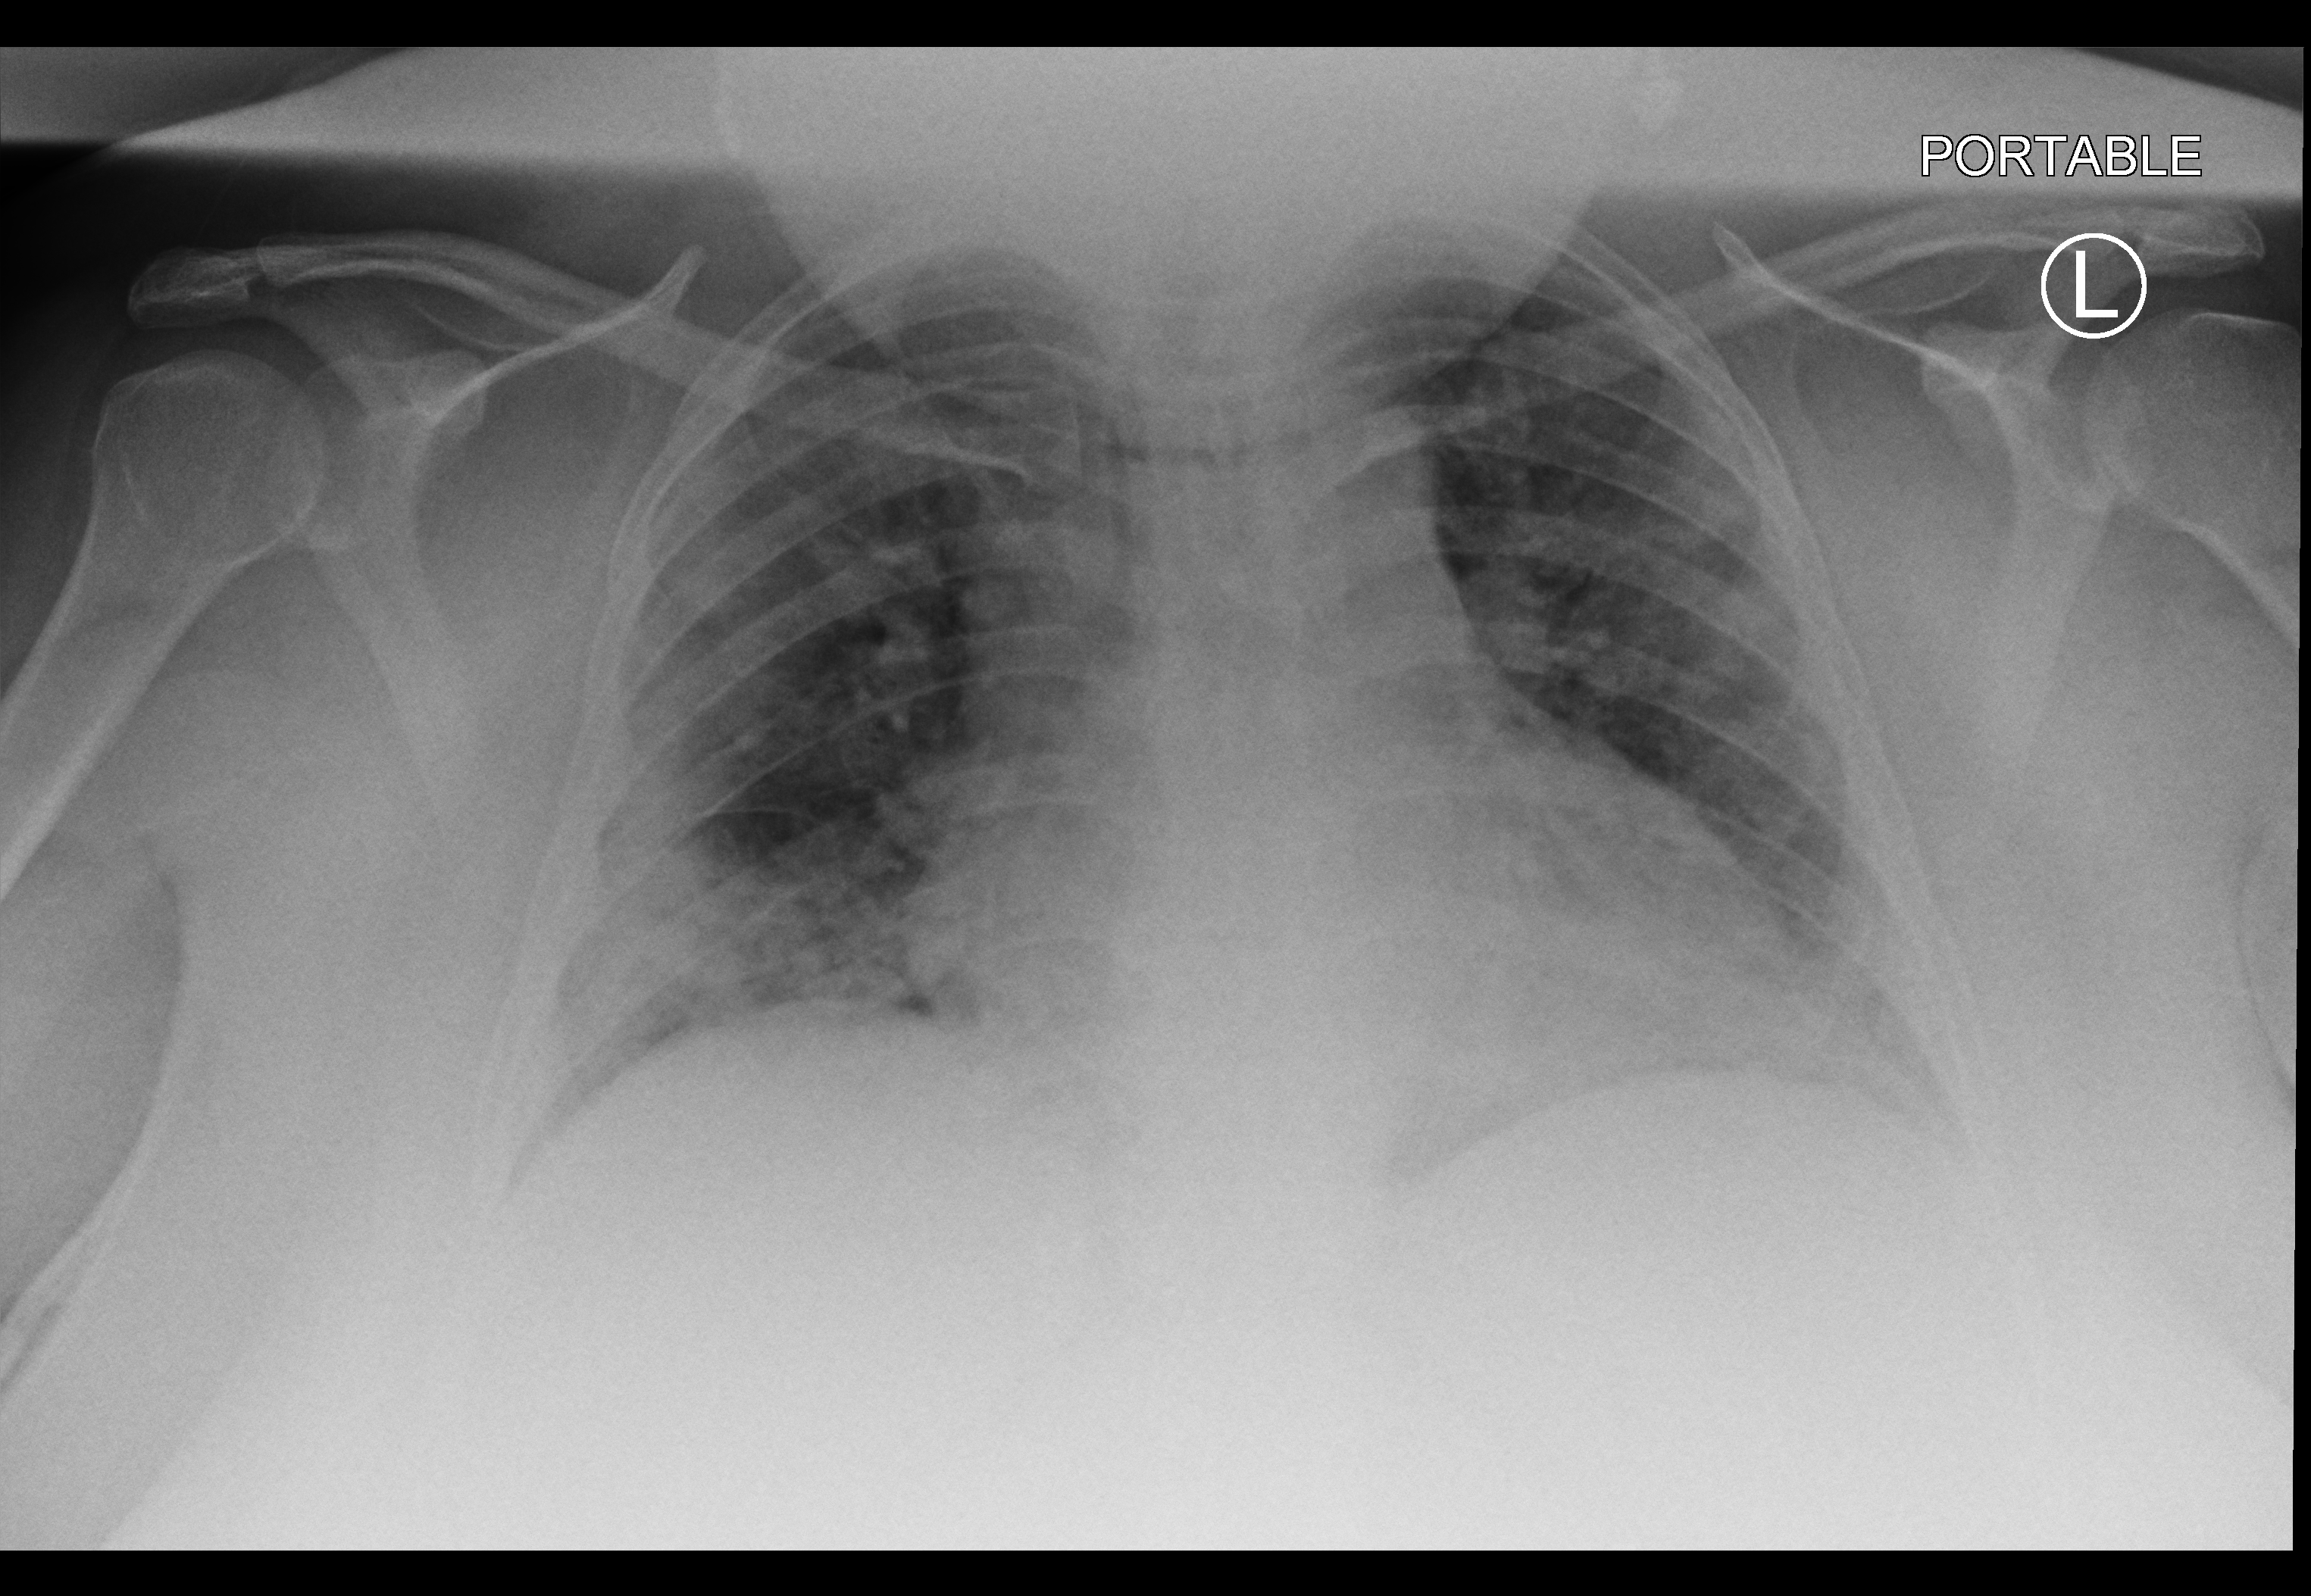
Portable chest radiograph, anteroposterior (AP) projection. Female patient hospitalised with COVID-19, age 18–59 years.
From the hospital-stay record, not from the radiograph (when in the stay this image was taken is not recorded): admitted to intensive care during this hospital stay: yes; other chronic lung disease (admission record): no.